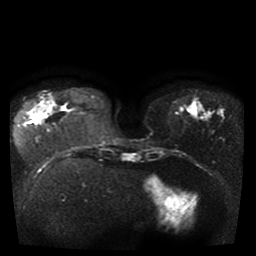
Breast MRI, one axial slice. Position 11 of 41 along the scan axis. Diffusion-weighted series; image 2 of 4 stored at this slice position (different b-values; order by instance number). 1.5 T. 256 × 256 image matrix. Female patient.
Outlined on this slice (expert manual segmentation):
- tumour on diffusion-weighted imaging: bounding box [x1, y1, x2, y2] px = [33, 104, 47, 113]